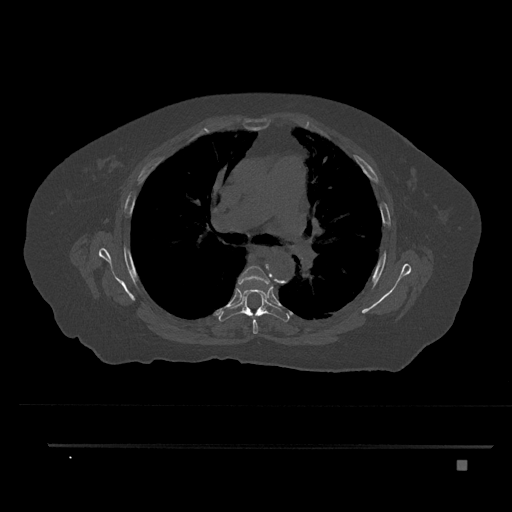
CT including the spine, one axial slice. Position 541 of 797 along the scan axis. Reconstruction kernel Br40s/3. Bone window (W 1800 / L 400 HU). 0.5 mm slice thickness. 512 × 512 image matrix, field of view 437 × 437 mm. Patient: female, 76 years. From the clinical record (not read from this slice): primary cancer: lung.
Outlined on this slice (semi-automatically segmented with operator editing):
- T5 vertebra: bounding box <238,265,270,334> (left, top, right, bottom; pixels)
- T6 vertebra: <218,281,290,322>